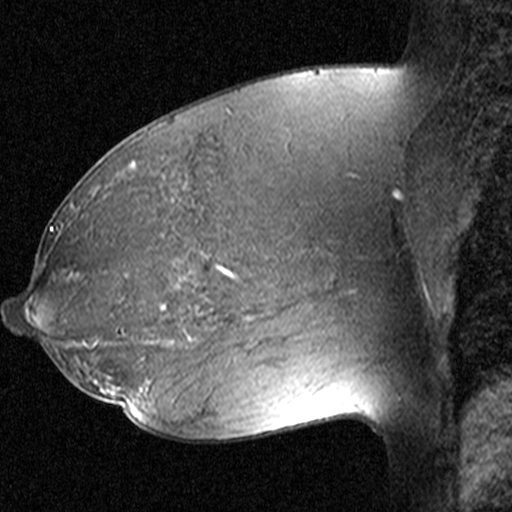
Breast MRI (dynamic contrast-enhanced), one sagittal slice. Slice 25 of 44 in the series (ordered by position). Dynamic contrast-enhanced study with each time point stored as its own series, time point 2 of 3 at this slice position (early post-contrast, ordered by acquisition time). 1.5 T. TE 4.5 ms, TR 11 ms. 3 mm slice thickness. 512 × 512 image matrix, field of view 200 × 200 mm. Patient: female, 38 years. From the clinical record (not read from this slice): setting: breast cancer imaged before/during neoadjuvant chemotherapy; receptor status: HR-positive, HER2-negative.
Structures marked on this image (semi-automatically segmented with operator editing):
- analysis volume of interest (the breast-tissue region the enhancement analysis was run in; not a lesion): bounding box (x1, y1, x2, y2) in pixels: (152, 236, 253, 335)
- tumour enhancement mask (voxels above the 90 % enhancement threshold inside the analysis volume of interest): (217, 266, 234, 277)